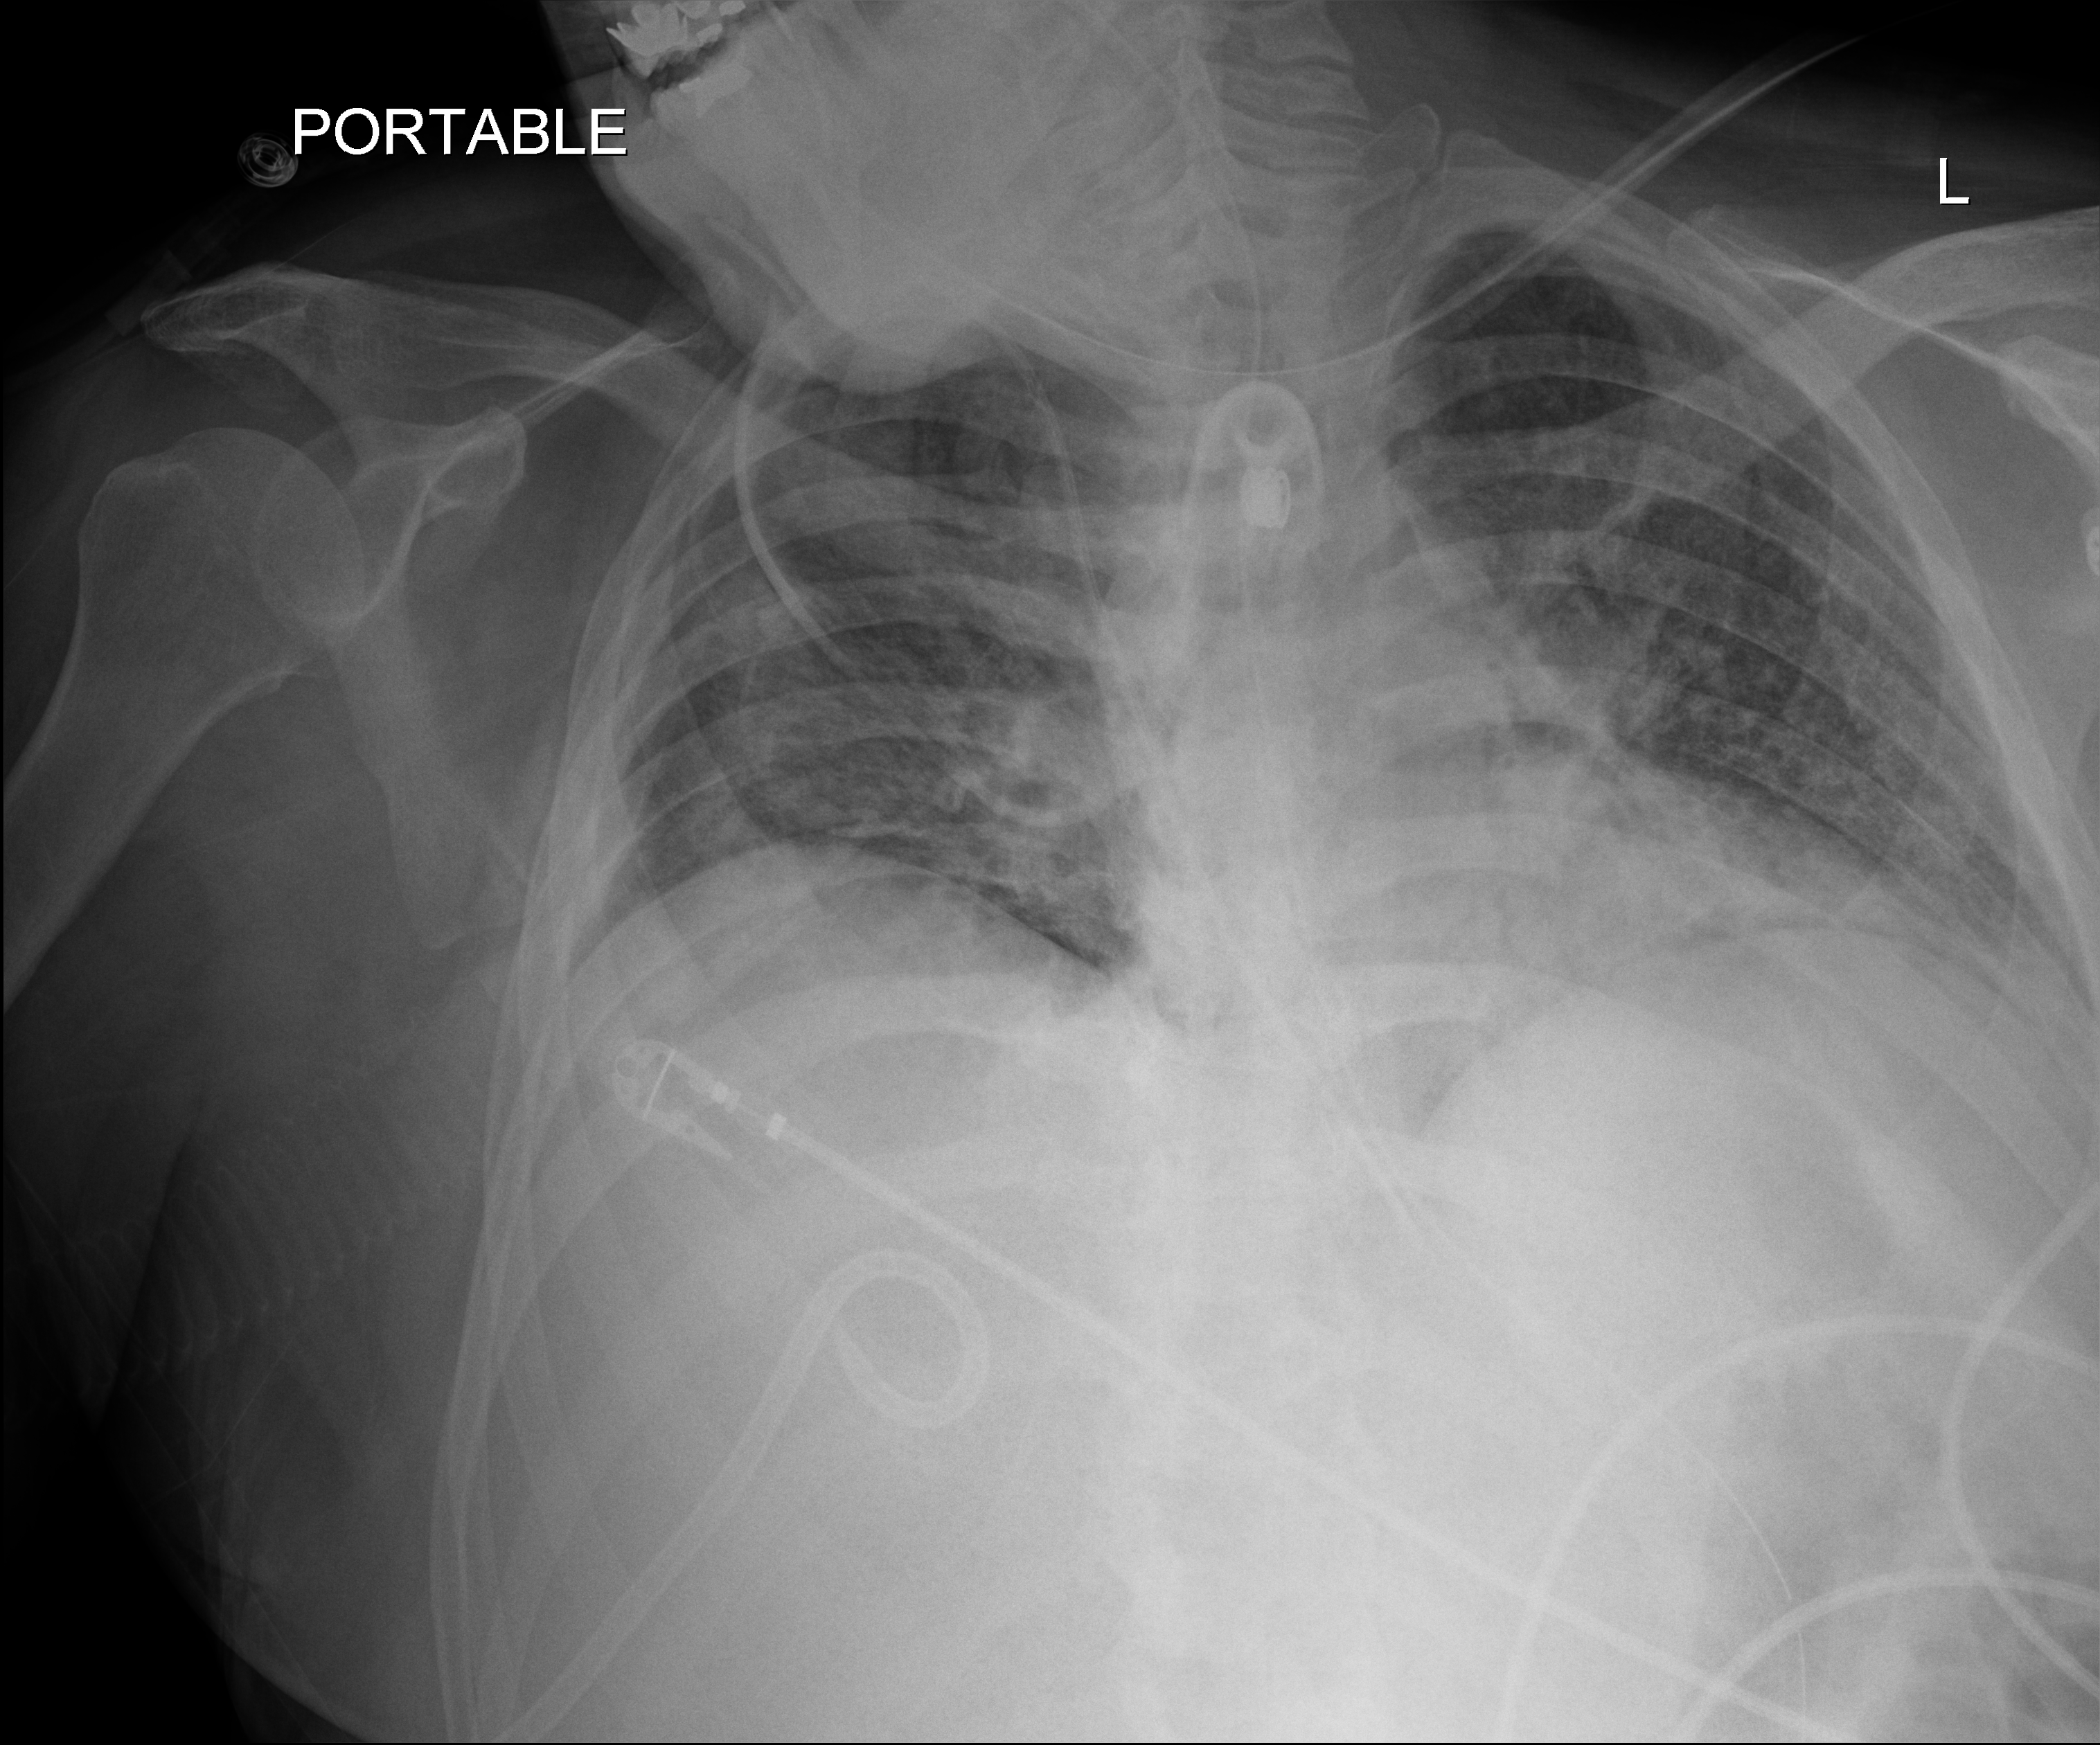
Portable chest radiograph; anteroposterior (AP) projection. Male patient hospitalised with COVID-19, age 18–59 years.
From the hospital-stay record, not from the radiograph (when in the stay this image was taken is not recorded): length of hospital stay: 80 days; smoking status (admission record): never; admitted to intensive care during this hospital stay: yes.